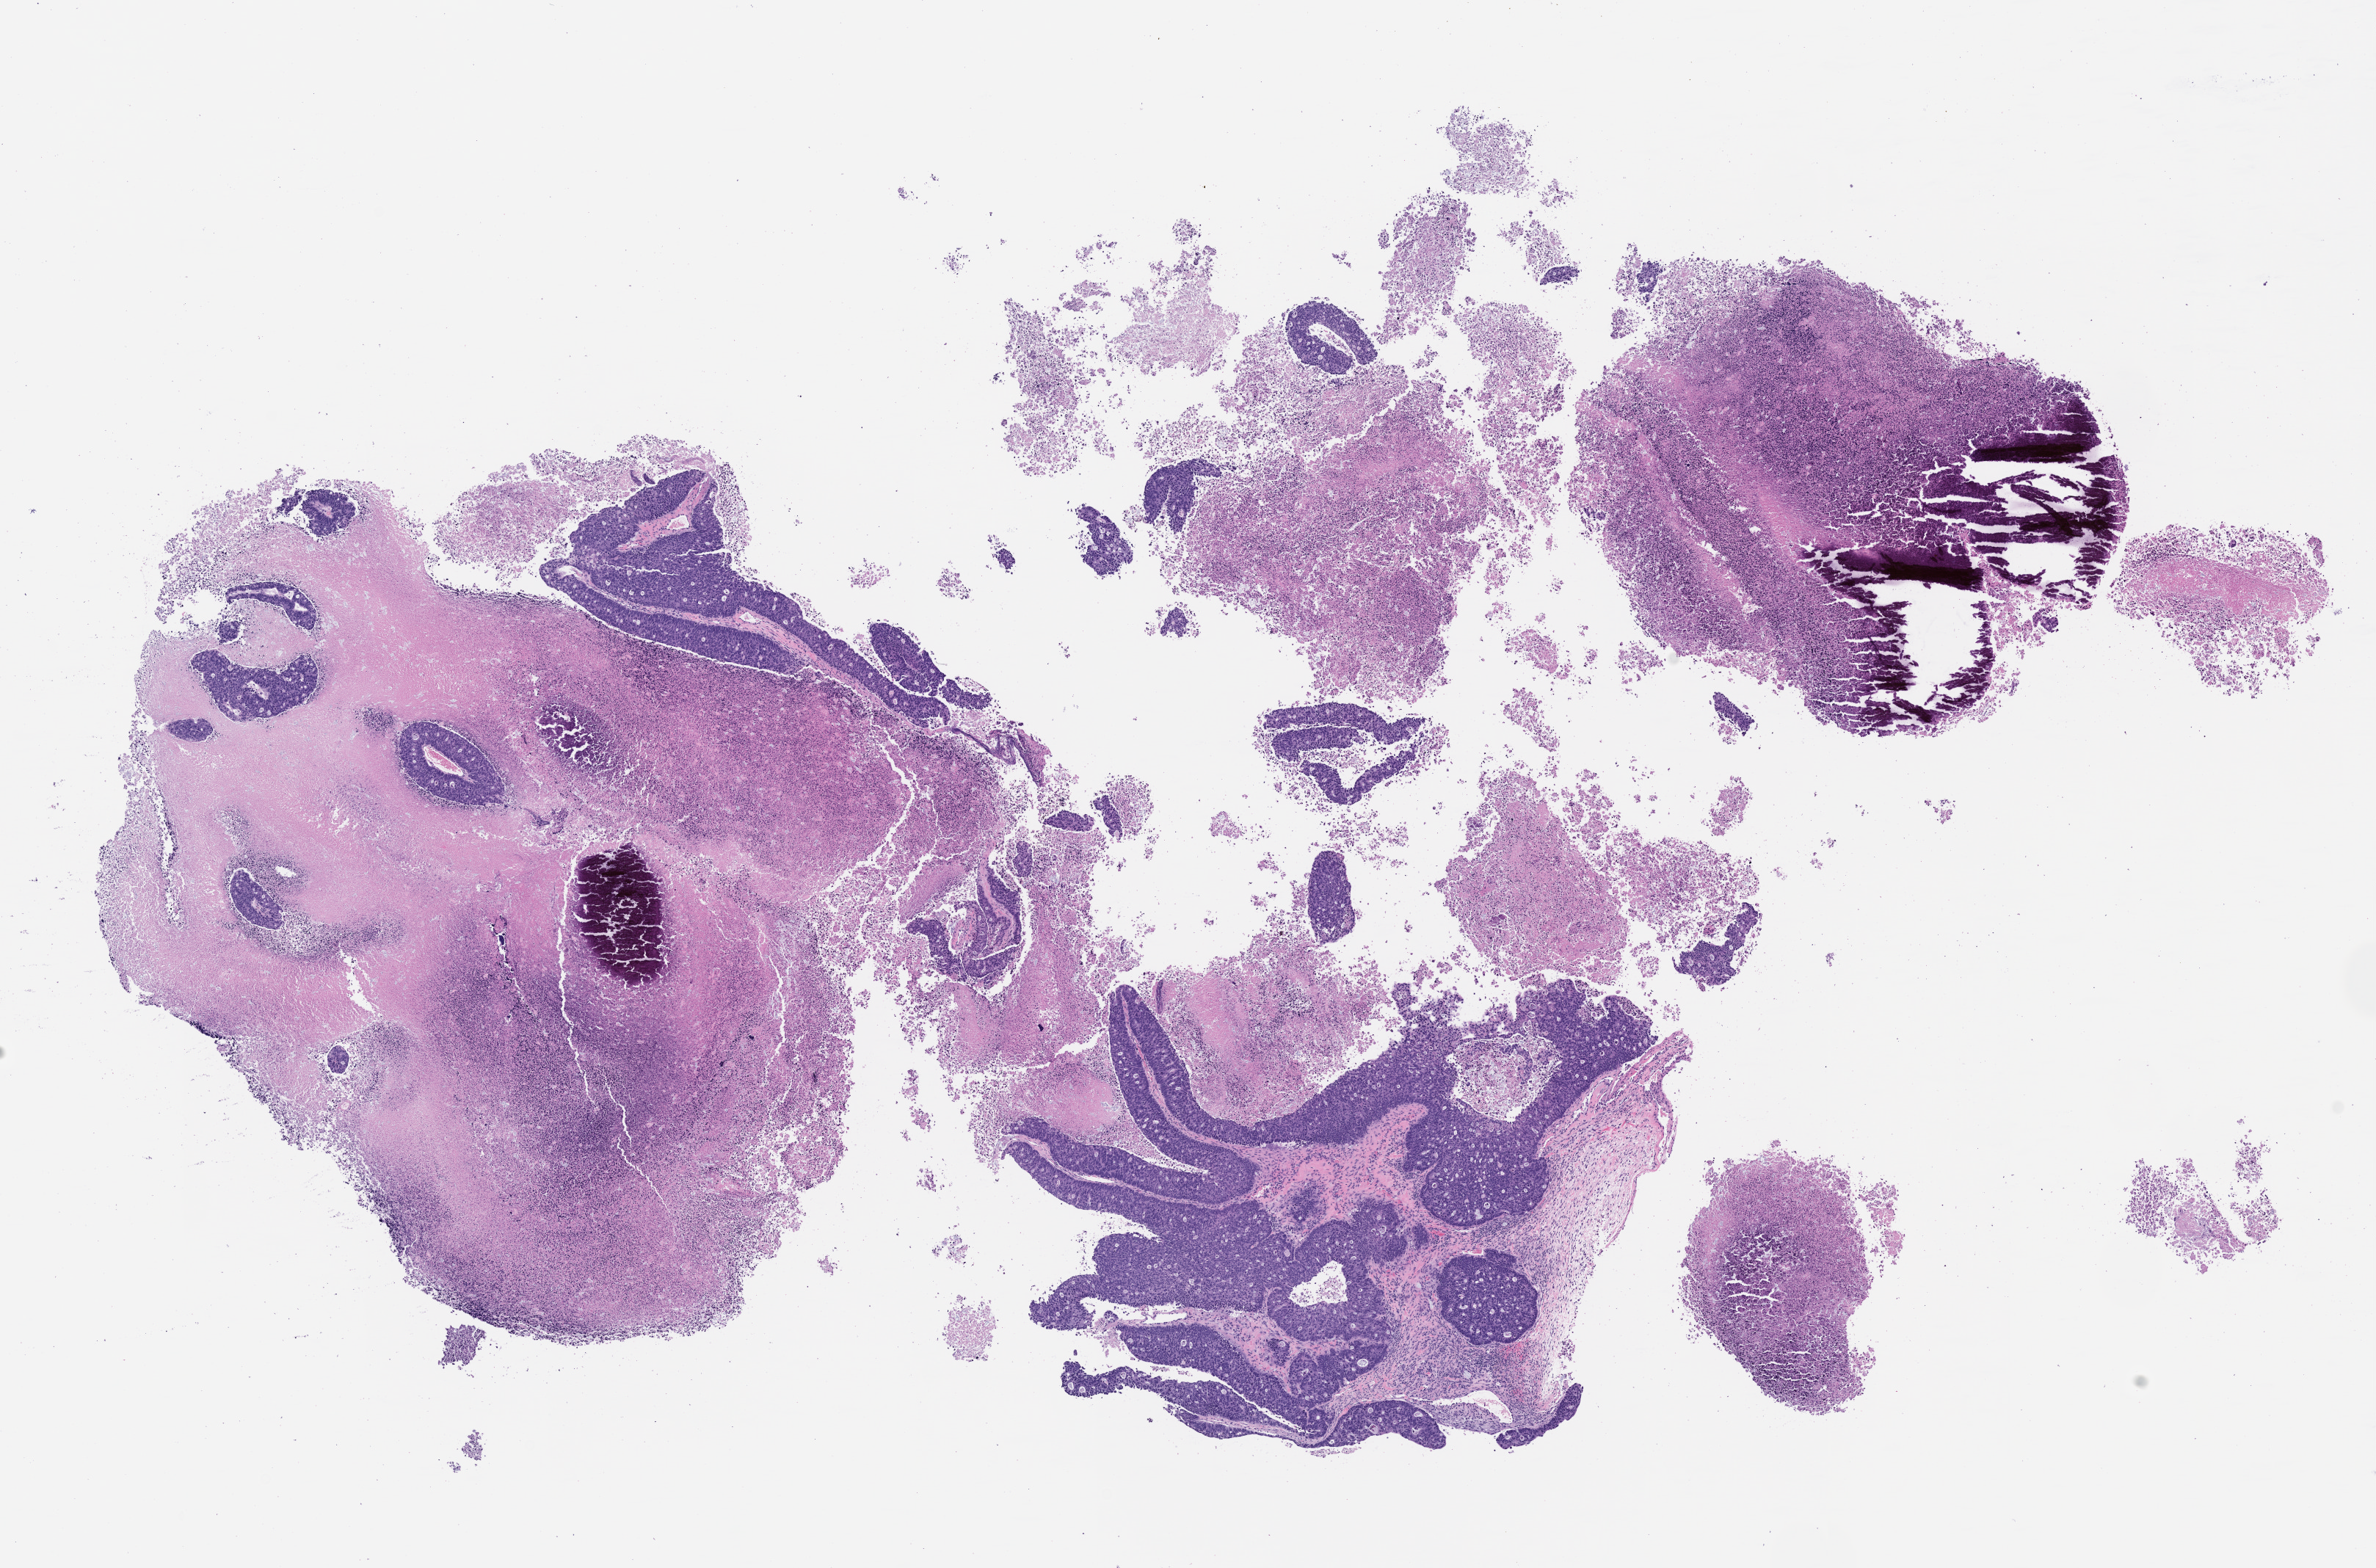
Whole-slide image, H&E: patient-derived xenograft (human tumor grown in a mouse), passage 2 — whole scanned area (about 13.0 x 8.6 mm) shown as a low-resolution overview; formalin-fixed paraffin-embedded section; originating tumor site category: rectum.
Originating patient diagnosis: Rectal Adenocarcinoma.